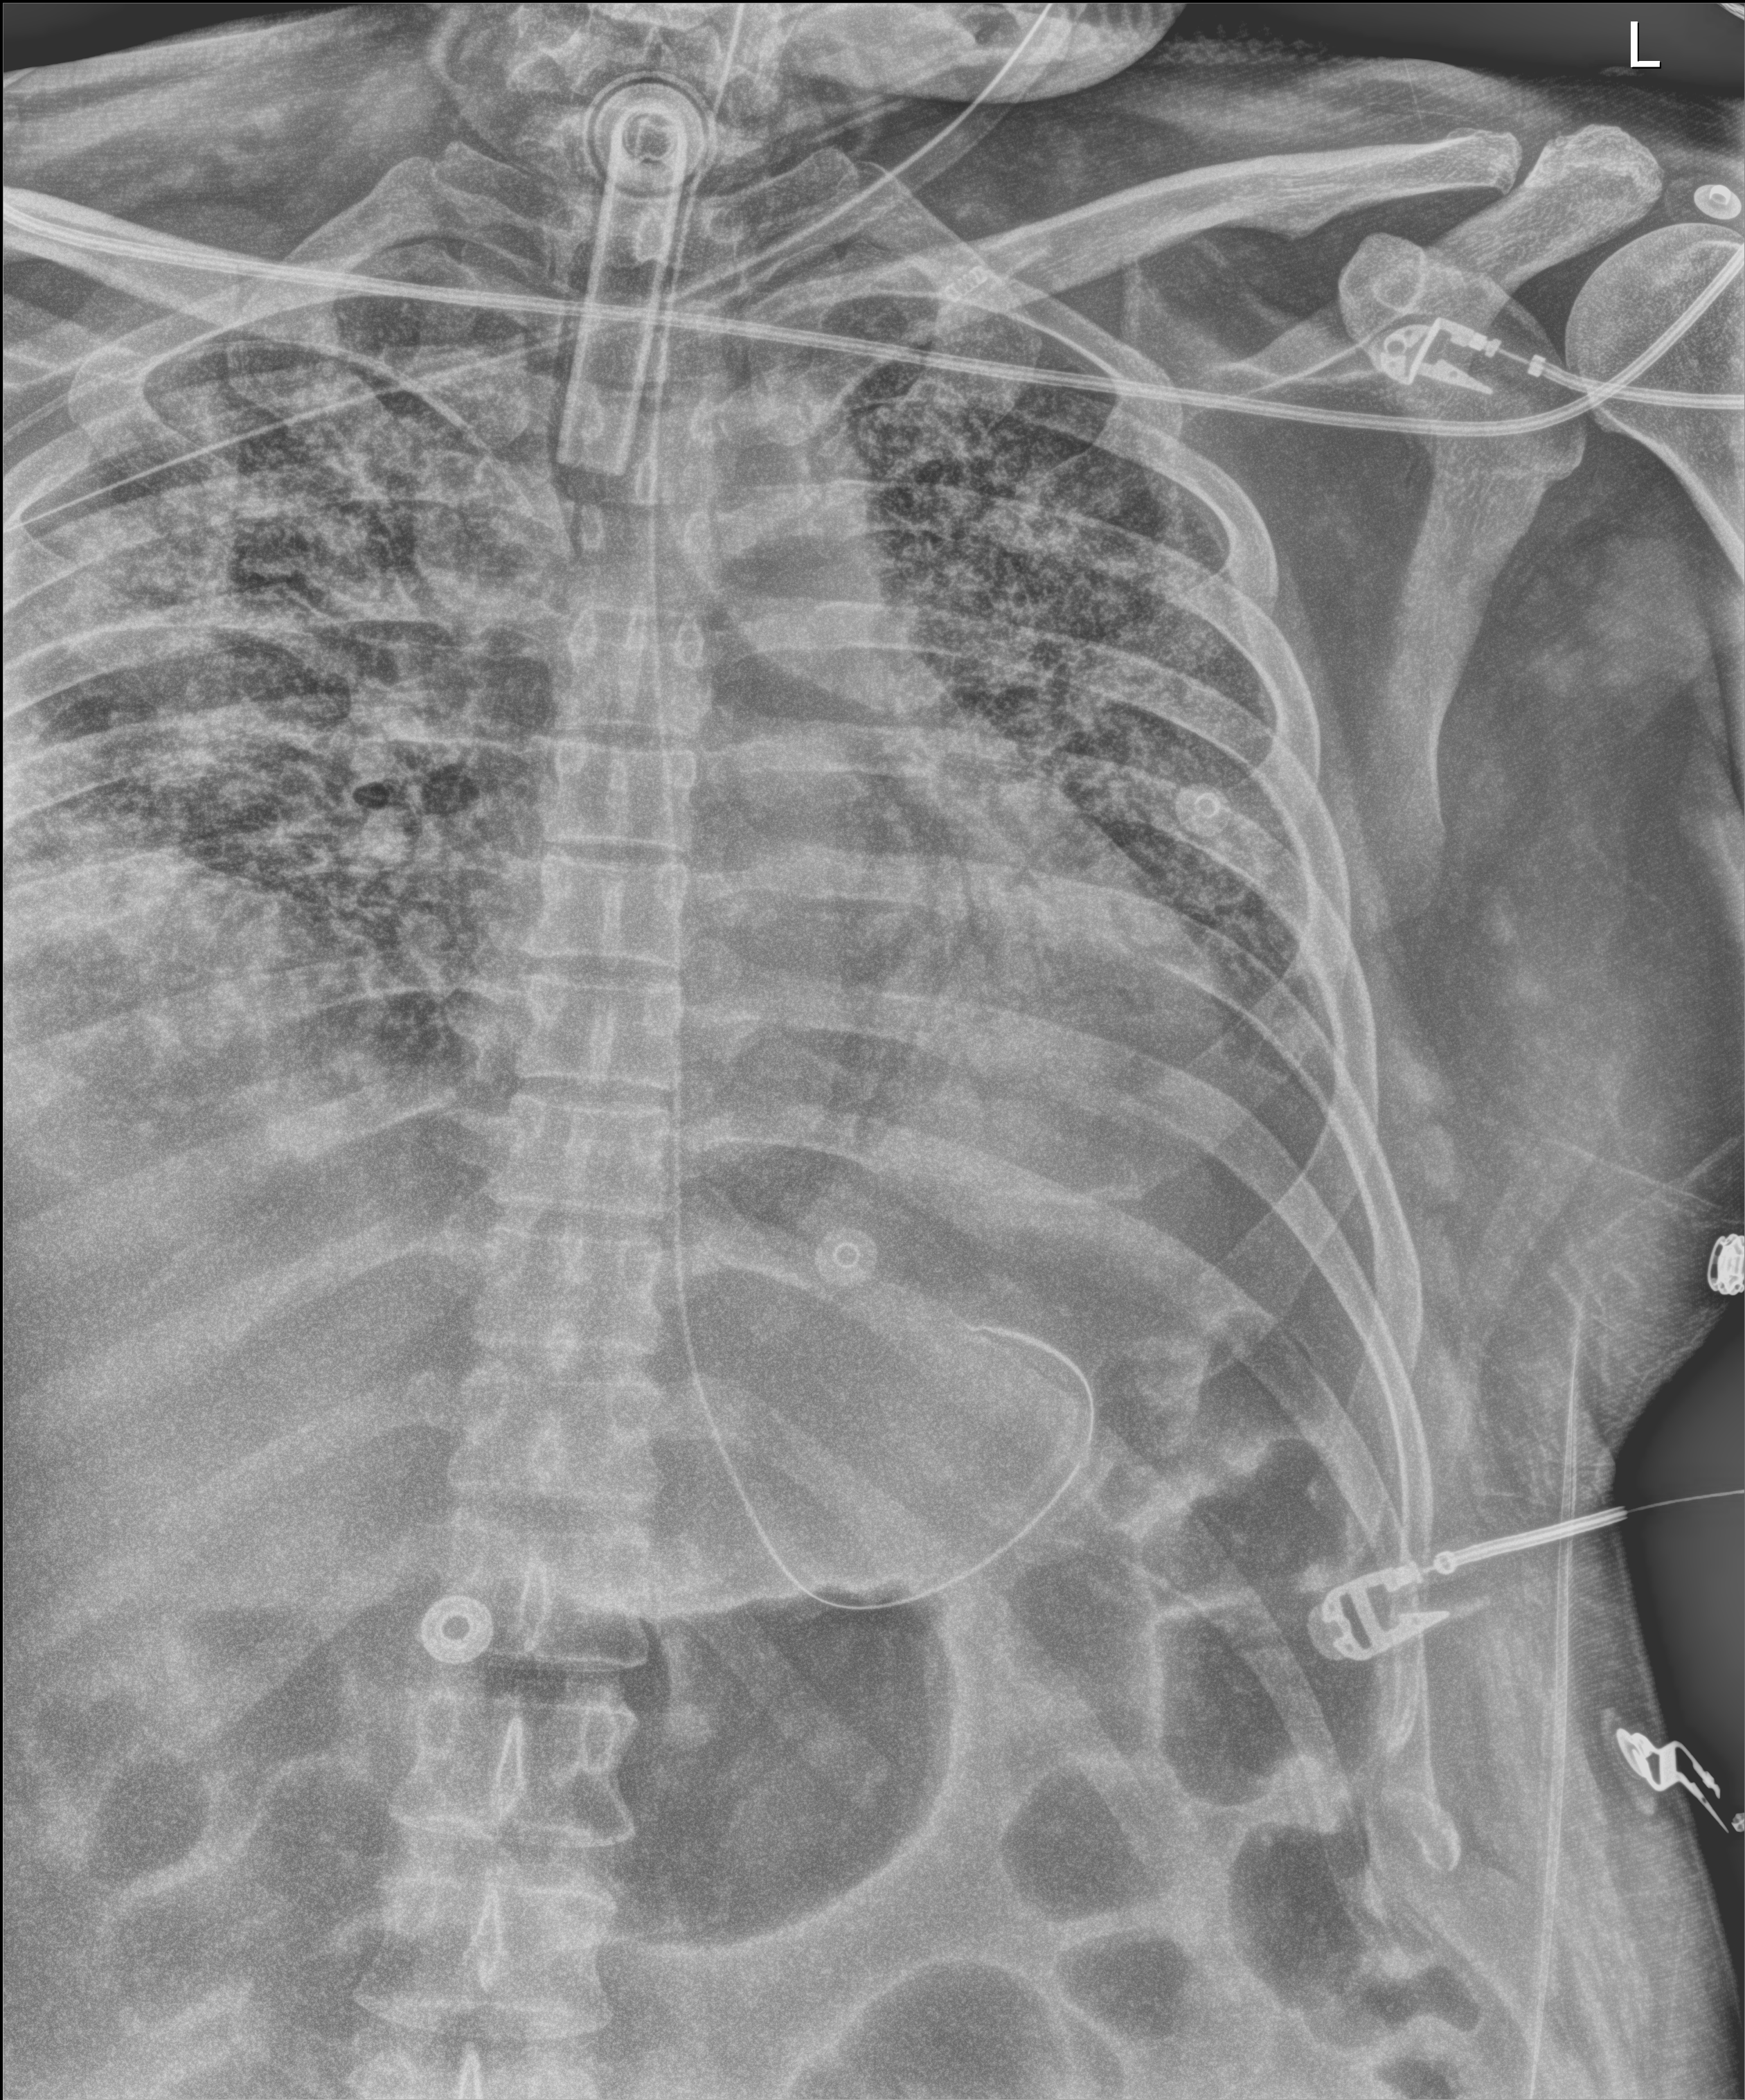
Chest X-ray (portable); anteroposterior (AP) projection. Male patient hospitalised with COVID-19, age 18–59 years.
Hospital-stay facts (about this admission, not read from this image; timing relative to this image not recorded): admitted to intensive care during this hospital stay: yes; diabetes (admission record): no; length of hospital stay: 96 days.